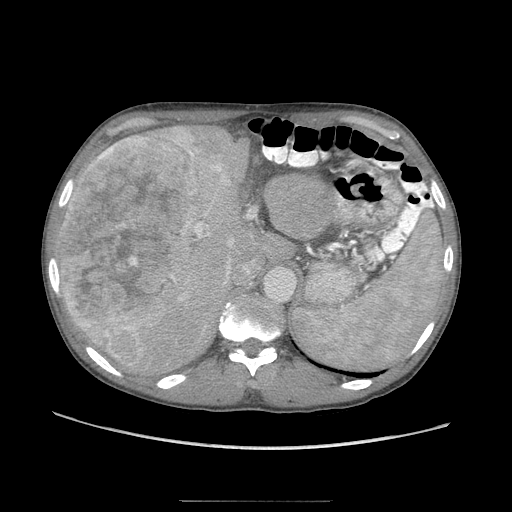
Contrast-enhanced abdominal CT (liver protocol), one axial slice; slice 66 of 103 in the series (ordered by position); 120 kVp; soft-tissue window (W 400 / L 40 HU); 2.5 mm slice thickness; 512 × 512 image matrix. Case-level facts recorded for this patient, not image findings: diagnosis: hepatocellular carcinoma (patient treated with transarterial chemoembolisation; whether this scan precedes or follows treatment is not stated here); TNM stage (as recorded): Stage-IIIA; Child-Pugh class: A; tumour differentiation: moderately differentiated.
Structures marked on this image (semi-automatically segmented with operator editing):
- liver parenchyma outside the tumour (the mass and vessels are separate outlines, so this box may not span the whole liver): bounding box <56,126,322,378> (left, top, right, bottom; pixels)
- mass: <61,136,235,365>
- liver vessels: <114,221,208,374>